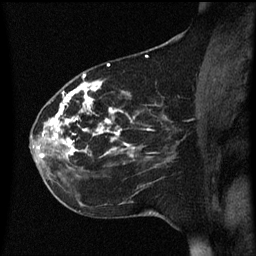
Breast MRI (dynamic contrast-enhanced), one sagittal slice. Position 26 of 60 along the scan axis. Dynamic contrast-enhanced series, image 2 of 3 at this slice position (ordered by acquisition). 1.5 T. TE 4.2 ms, TR 8.4 ms. 256 × 256 image matrix, field of view 200 × 200 mm. Female patient, age 35 years. Case-level facts recorded for this patient, not image findings: setting: breast cancer imaged before/during neoadjuvant chemotherapy; receptor status: HER2-positive.
Annotated regions visible in this slice (semi-automatically segmented with operator editing):
- analysis volume of interest (the breast-tissue region the enhancement analysis was run in; not a lesion): bounding box <32,78,173,163> (left, top, right, bottom; pixels)
- tumour enhancement mask (voxels above the 70 % enhancement threshold inside the analysis volume of interest): <38,80,133,157>